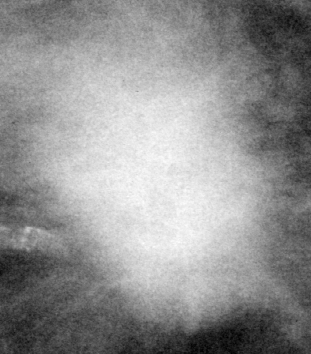
Cropped region of a digitized screen-film mammogram centred on a radiologist-marked abnormality; right breast; CC view; BI-RADS breast density category 3 (scale 1–4).
Mass, shape irregular / architectural distortion, margins spiculated; BI-RADS assessment category 5; subtlety rating 5 on a 1 (subtle) to 5 (obvious) scale; pathology result (as recorded, not read from the image): malignant.